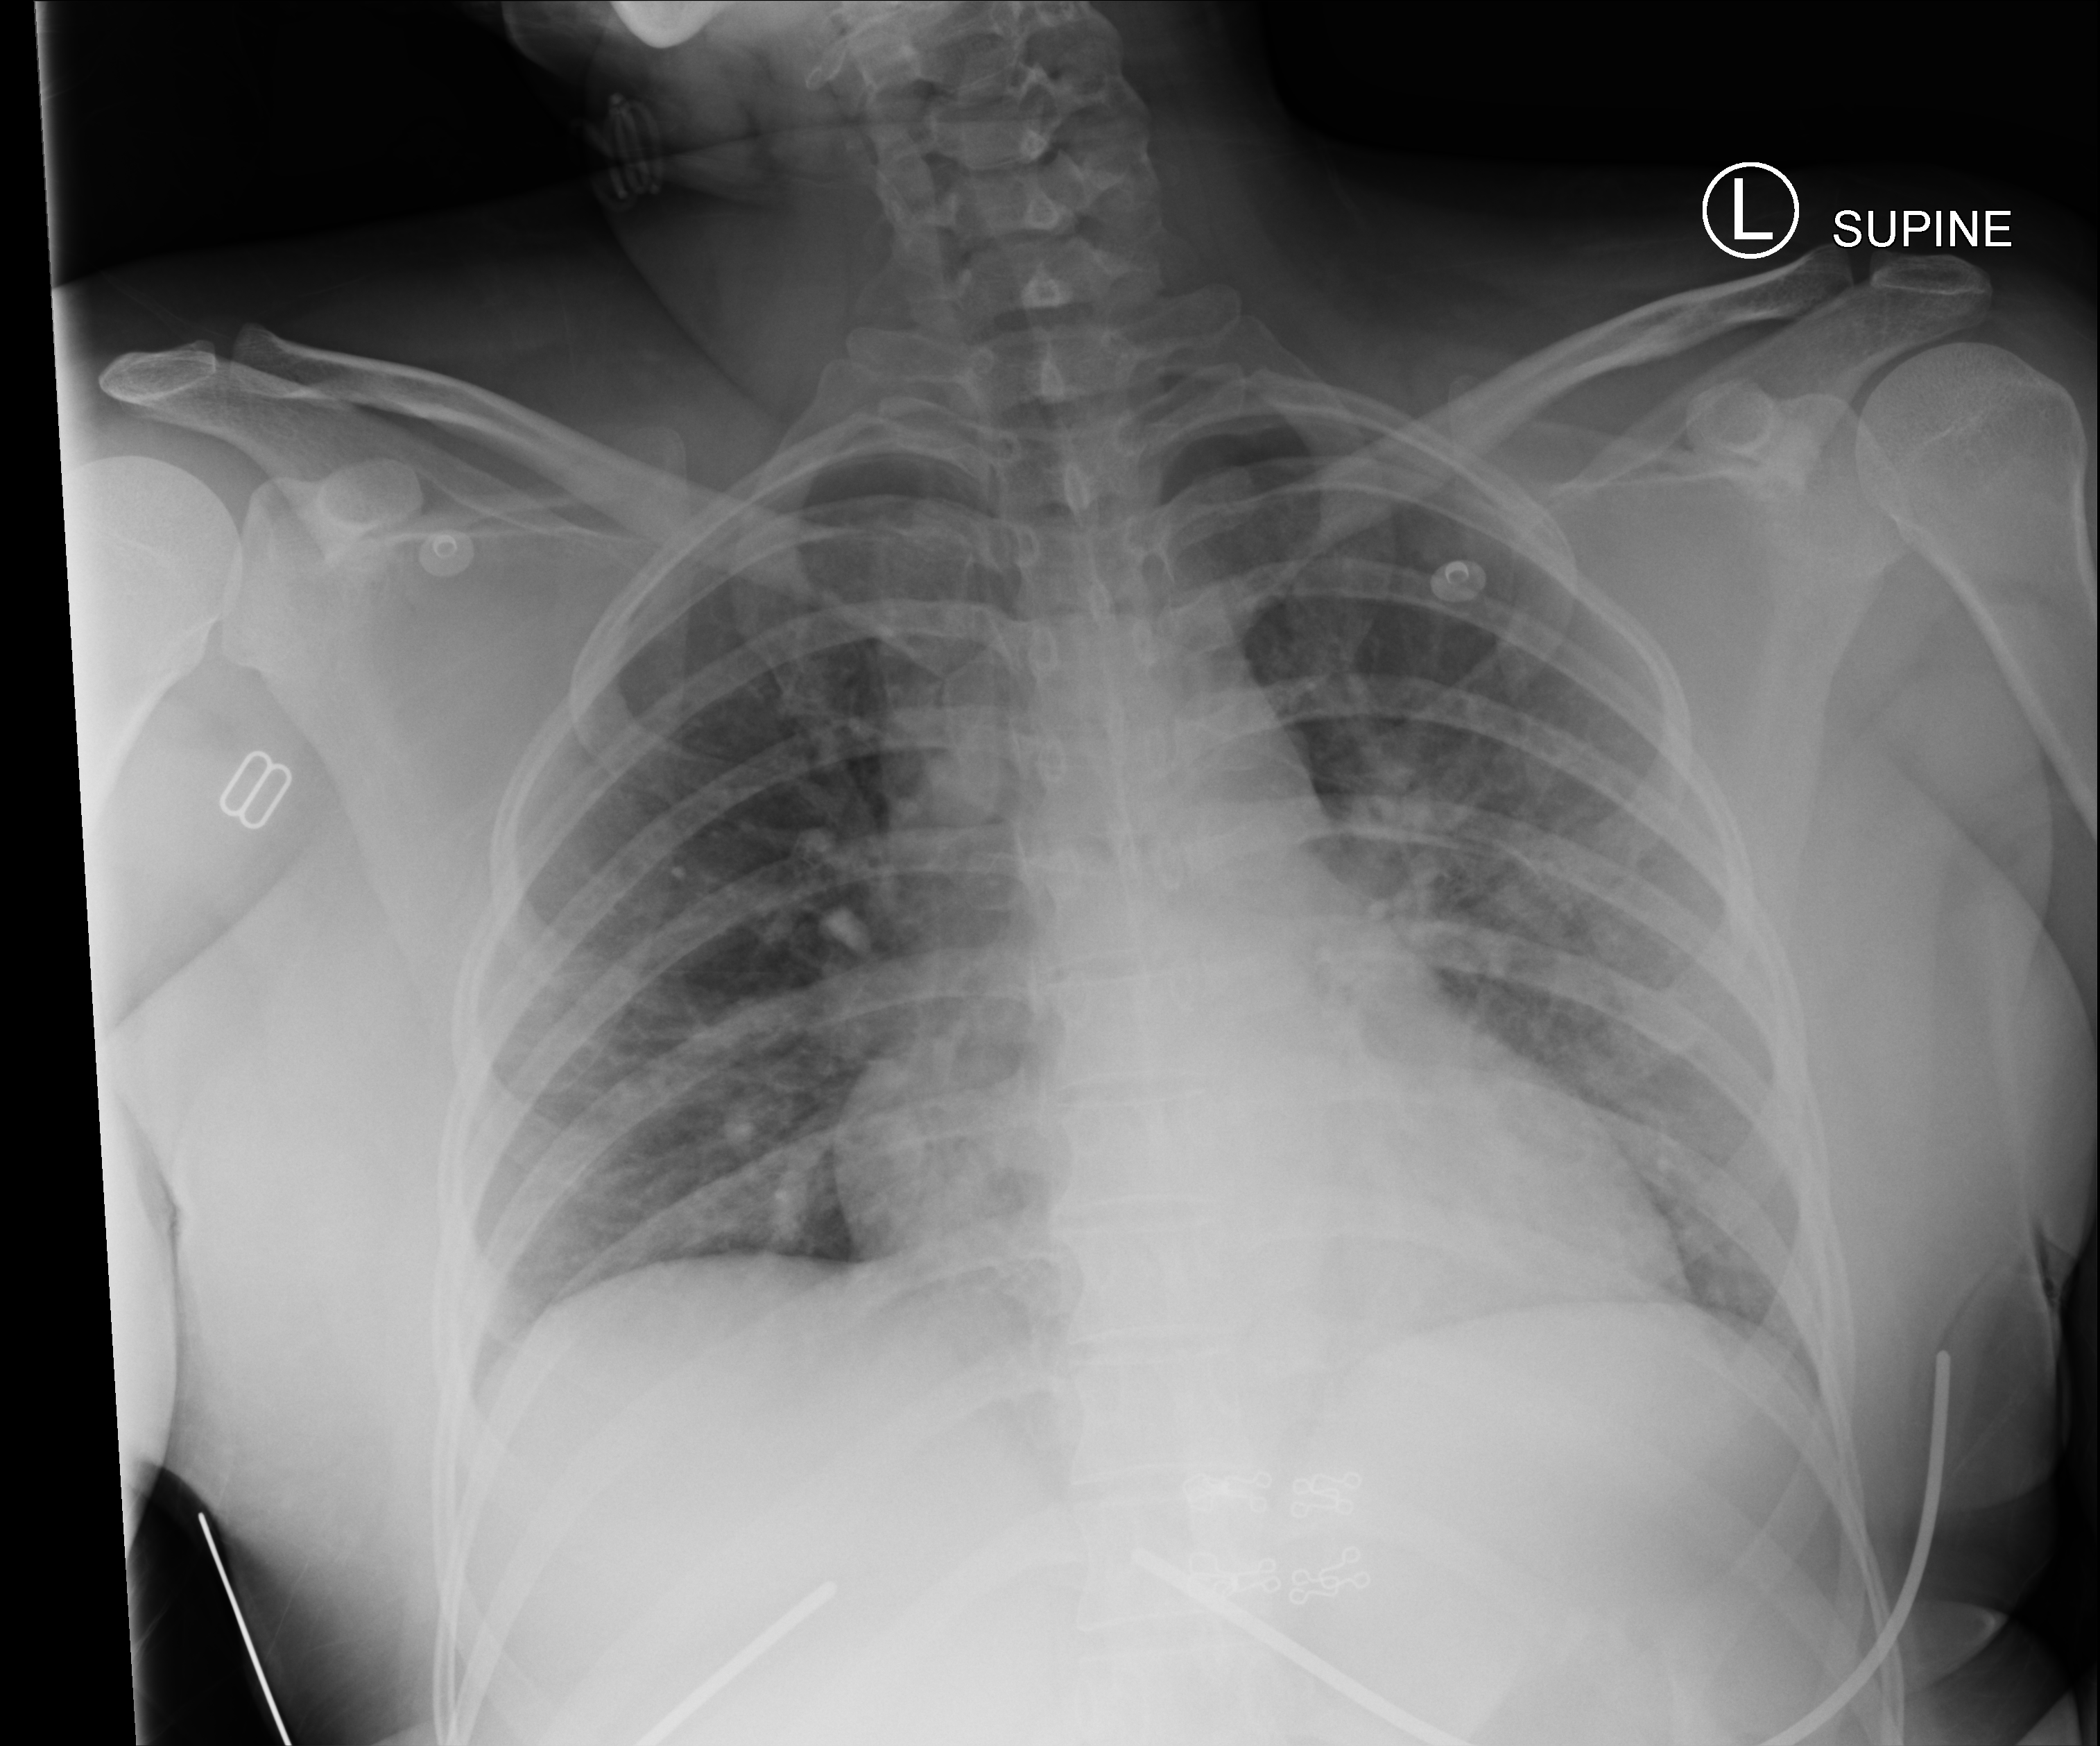
Chest X-ray (portable); anteroposterior (AP) projection. Female patient hospitalised with COVID-19, age 18–59 years.
Hospital-stay facts (about this admission, not read from this image; timing relative to this image not recorded): mechanically ventilated during this hospital stay: no.